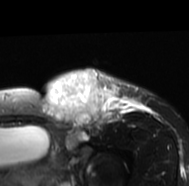
MRI of an extremity soft-tissue mass, one axial slice. Slice 54 of 77 in the series (ordered by position). T2-weighted fat-saturated. MR volume resampled by the dataset authors to the PET/CT grid (not the native acquisition matrix). 3.27 mm slice thickness. 189 × 186 image matrix, field of view 185 × 182 mm. Female patient. Case-level facts recorded for this patient, not image findings: histological type: leiomyosarcoma; grade: high; site of the primary tumour: groin.
Outlined on this slice (expert contour drawn on MRI and transferred to this co-registered scan by the dataset authors):
- gross tumour volume including surrounding oedema: bounding box [x1, y1, x2, y2] px = [42, 68, 151, 140]
- gross tumour volume (mass): [42, 70, 109, 128]